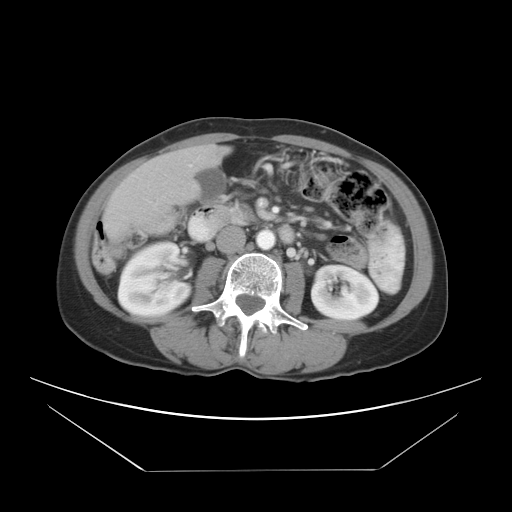
Contrast-enhanced abdominal CT, one axial slice; position 9 of 30 along the scan axis; 120 kVp; intravenous contrast given; soft-tissue window (W 400 / L 40 HU); 7.5 mm slice thickness; 512 × 512 image matrix. Female patient, age 54 years. From the clinical record (not read from this slice): diagnosis: colorectal cancer liver metastases, imaged before liver resection; multiple liver metastases: yes; largest metastasis: 2.5 cm; disease in both lobes: yes.
Annotated regions visible in this slice (manually delineated by an expert):
- liver: bounding box (x1, y1, x2, y2) in pixels: (105, 148, 225, 239)
- planned liver remnant (the part of the liver to remain after resection): (125, 148, 224, 206)
- liver metastasis: (111, 216, 116, 222)